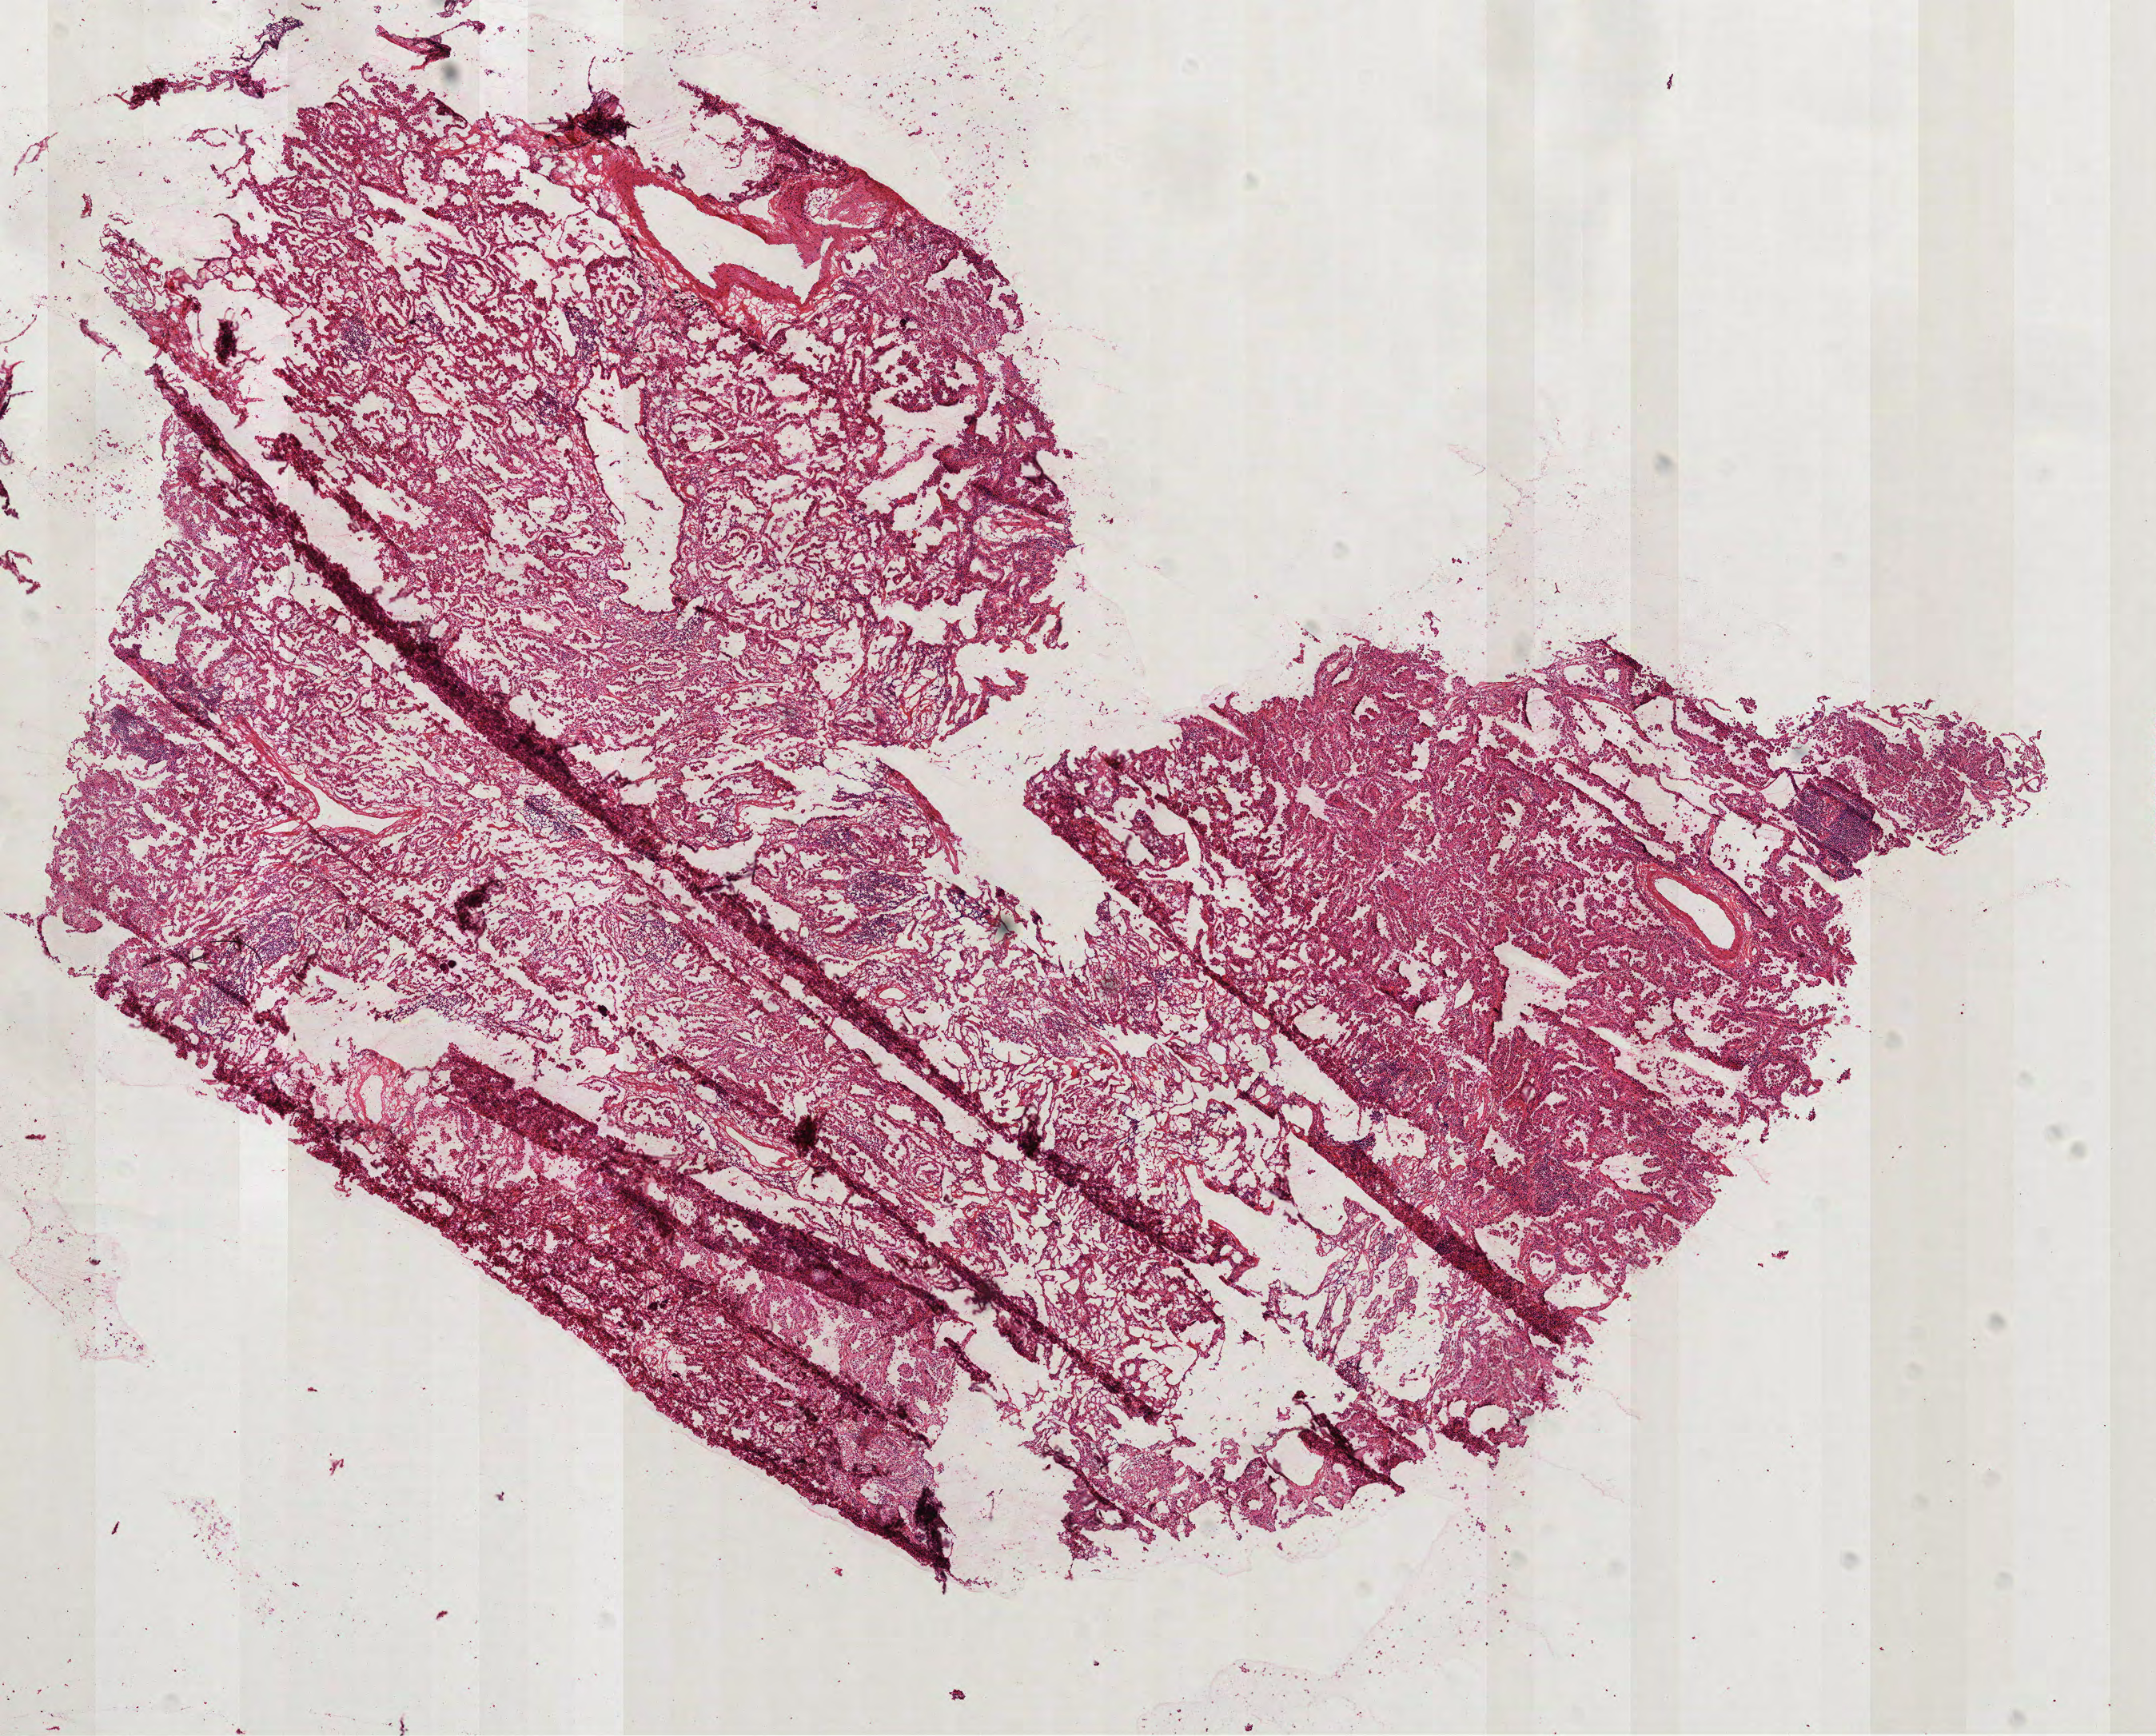
Whole-slide histology image, H&E-stained — a low-resolution overview of the entire scanned area, about 10.9 x 8.8 mm (acquisition: 40x scan); frozen section; lung, primary tumour sample. Patient: male, age at initial diagnosis 74 years. Slide review estimates, as recorded: tumour cells 85%, tumour nuclei 80%, normal cells 0%, stromal cells 15%, necrosis 0%.
Diagnosis: Papillary adenocarcinoma, NOS (upper lobe, lung). AJCC pathologic stage: IA (7th edition).